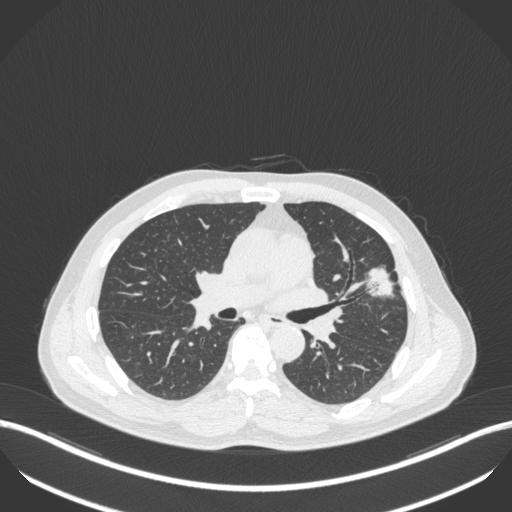
Chest CT, one axial slice; slice 225 of 418 in the series (ordered by position); 120 kVp; lung window (W 1500 / L -600 HU); 512 × 512 image matrix, field of view 400 × 400 mm. Male patient, age 55 years. Case-level facts recorded for this patient, not image findings: clinical TNM (as recorded): T1c N0 M0.
Annotated regions visible in this slice (rectangle marked by the reading radiologist):
- lung tumour (recorded histology: adenocarcinoma): bounding box <361,263,399,300> (left, top, right, bottom; pixels)